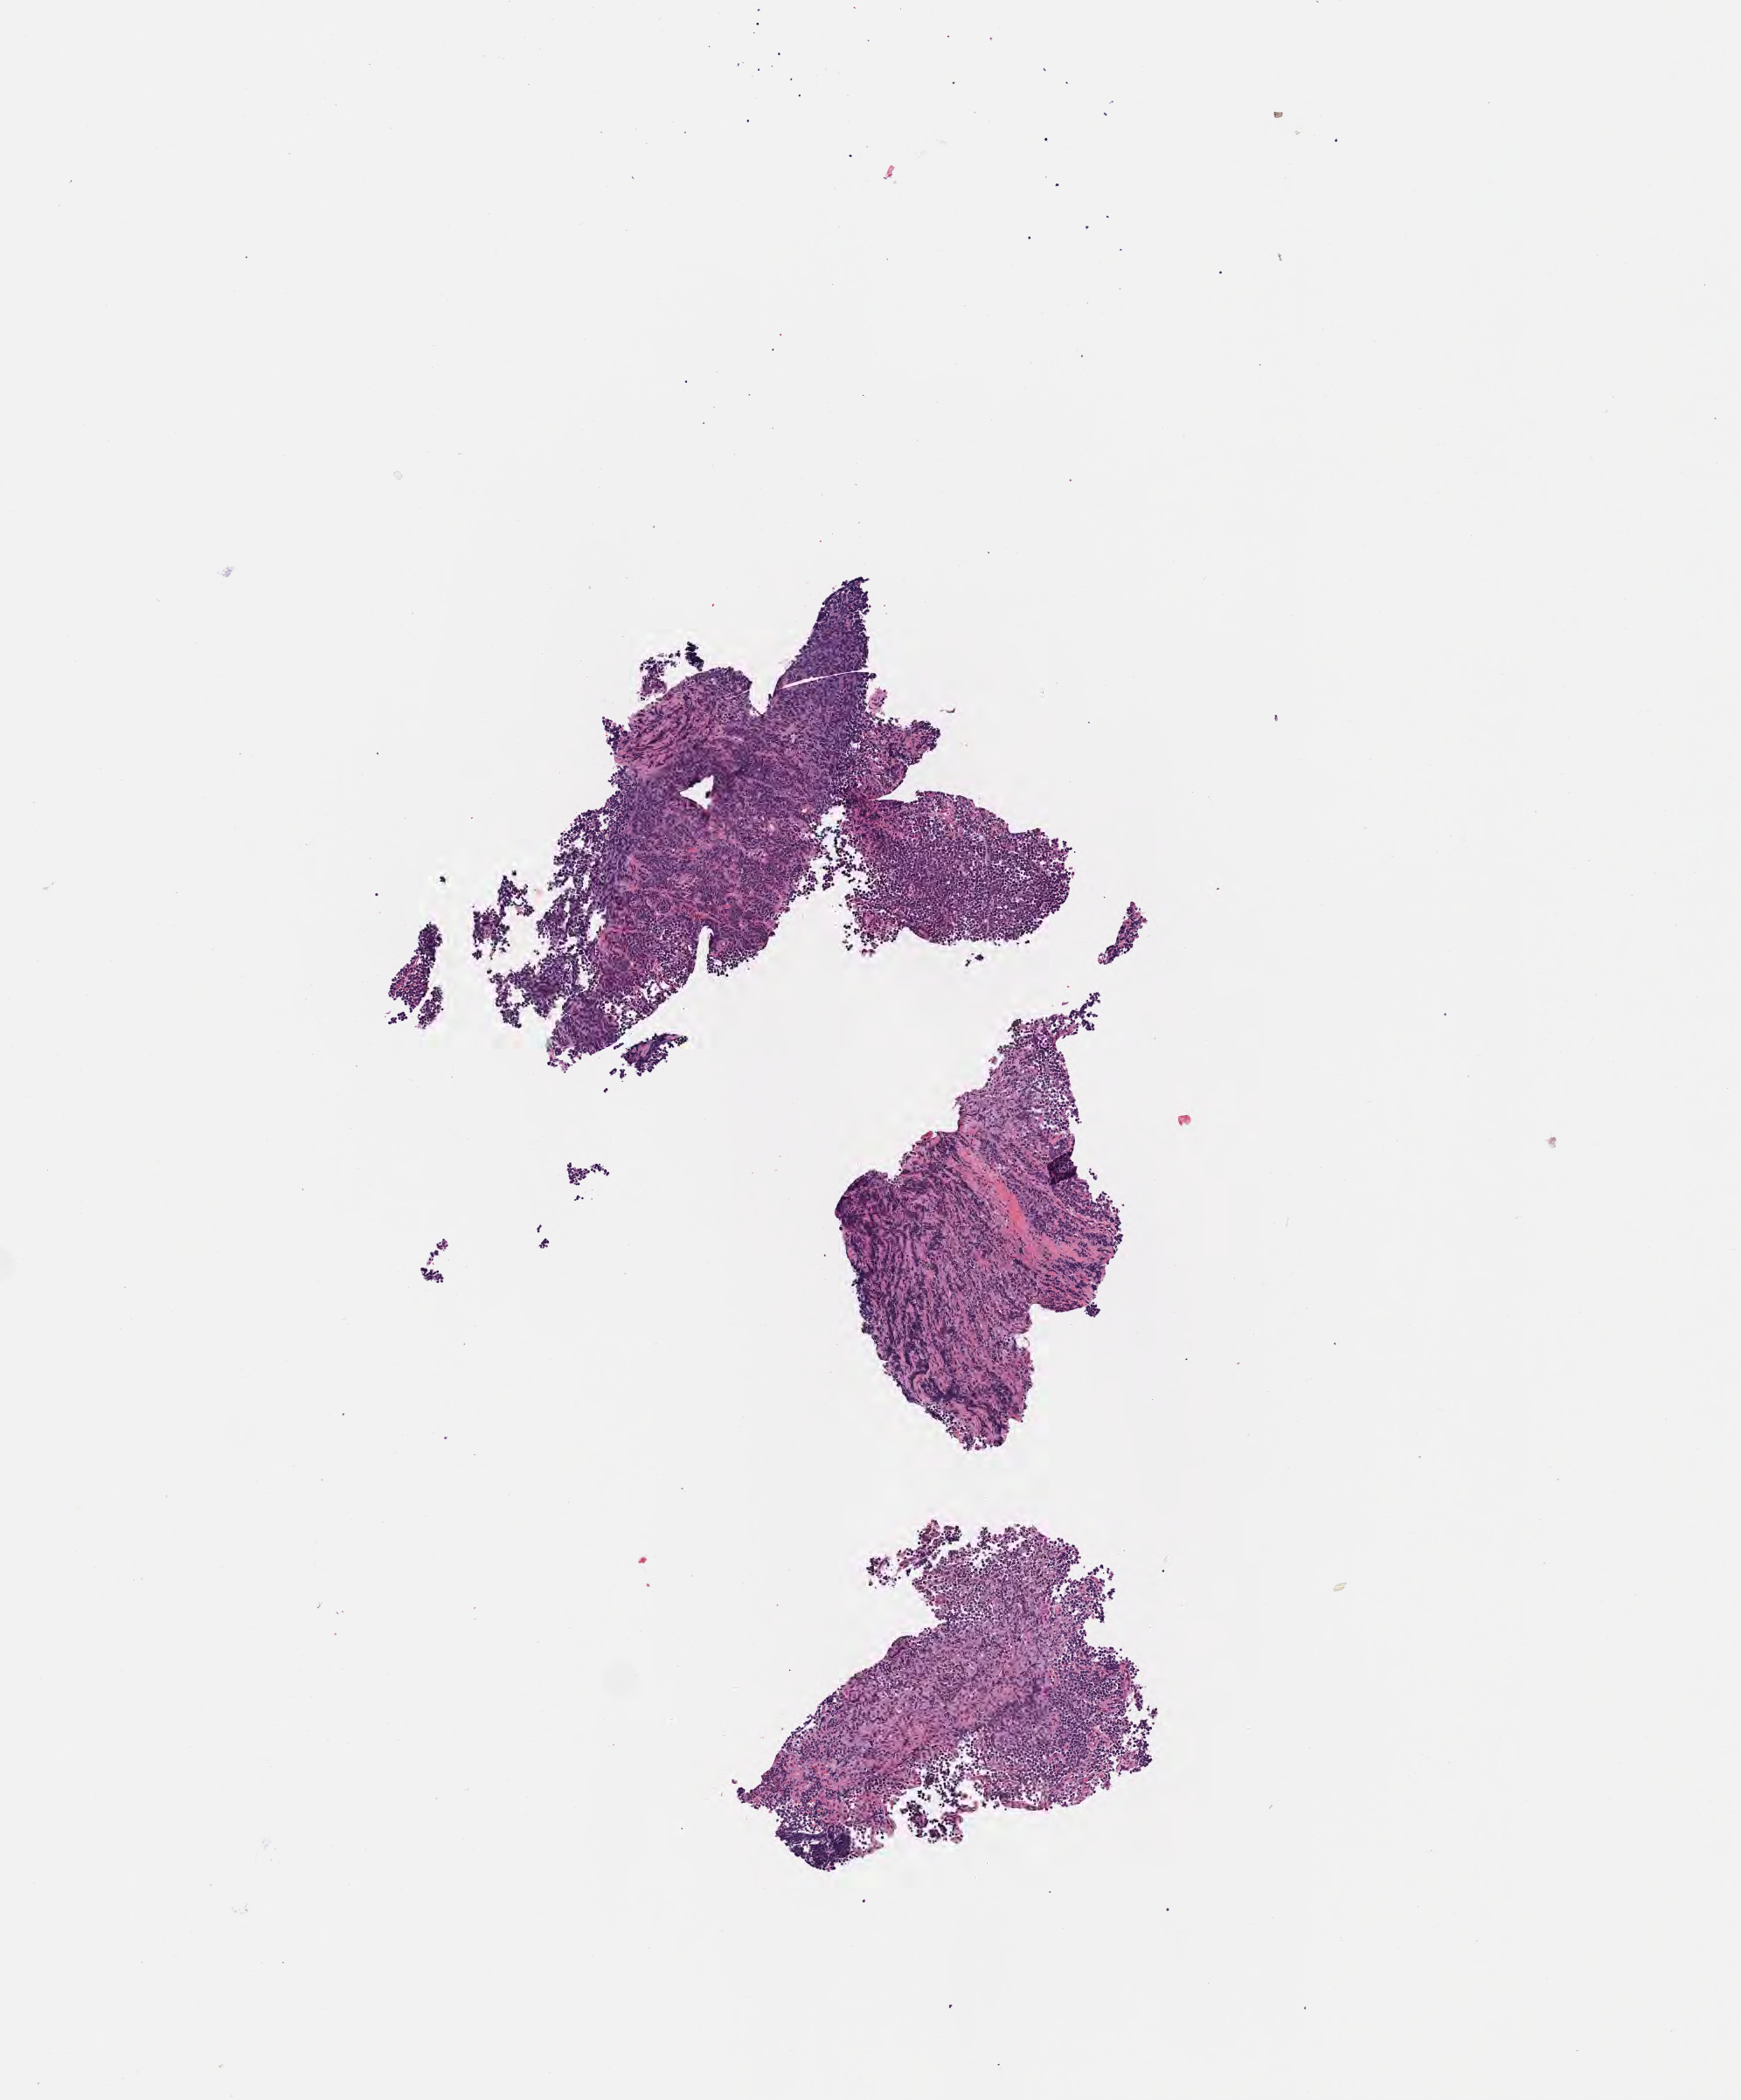
Haematoxylin and eosin whole-slide image, low-resolution overview of the scanned area, about 4.0 x 4.9 mm; specimen: tumor tissue; anatomic site: abdomen proper. Male patient; age at initial diagnosis 6 years.
Diagnosis: Burkitt lymphoma, NOS.